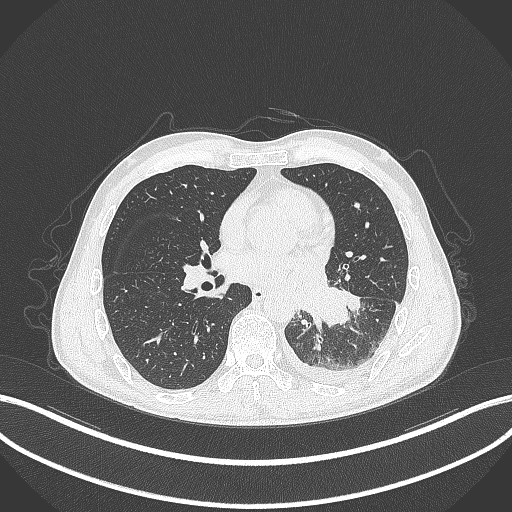
Chest CT, one axial slice. Slice 144 of 295 in the series (ordered by position). Reconstruction kernel B70f. 120 kVp. Lung window (W 1500 / L -600 HU). 512 × 512 image matrix, field of view 400 × 400 mm. Patient: male, 47 years. From the clinical record (not read from this slice): clinical TNM (as recorded): T3 N1 M1c; histopathological grade: G3.
Outlined on this slice (bounding box drawn by a radiologist):
- lung tumour (recorded histology: small cell carcinoma): box from (x=307, y=283) to (x=349, y=329) px